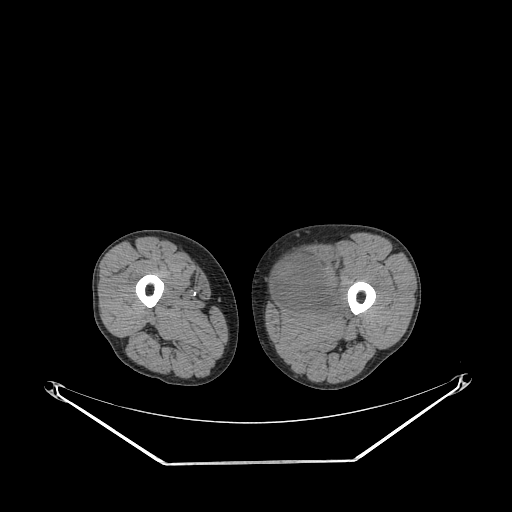
CT of an extremity soft-tissue mass (from a PET/CT study), one axial slice. Slice 232 of 267 in the series (ordered by position). Reconstruction kernel STANDARD. 140 kVp. Soft-tissue window (W 400 / L 40 HU). 512 × 512 image matrix, field of view 500 × 500 mm. Male patient. From the clinical record (not read from this slice): histological type: pleiomorphic liposarcoma; grade: high; site of the primary tumour: left thigh.
Annotated regions visible in this slice (expert contour drawn on MRI and transferred to this co-registered scan by the dataset authors):
- gross tumour volume including surrounding oedema: bounding box <274,251,344,320> (left, top, right, bottom; pixels)
- gross tumour volume (mass): <274,253,337,312>